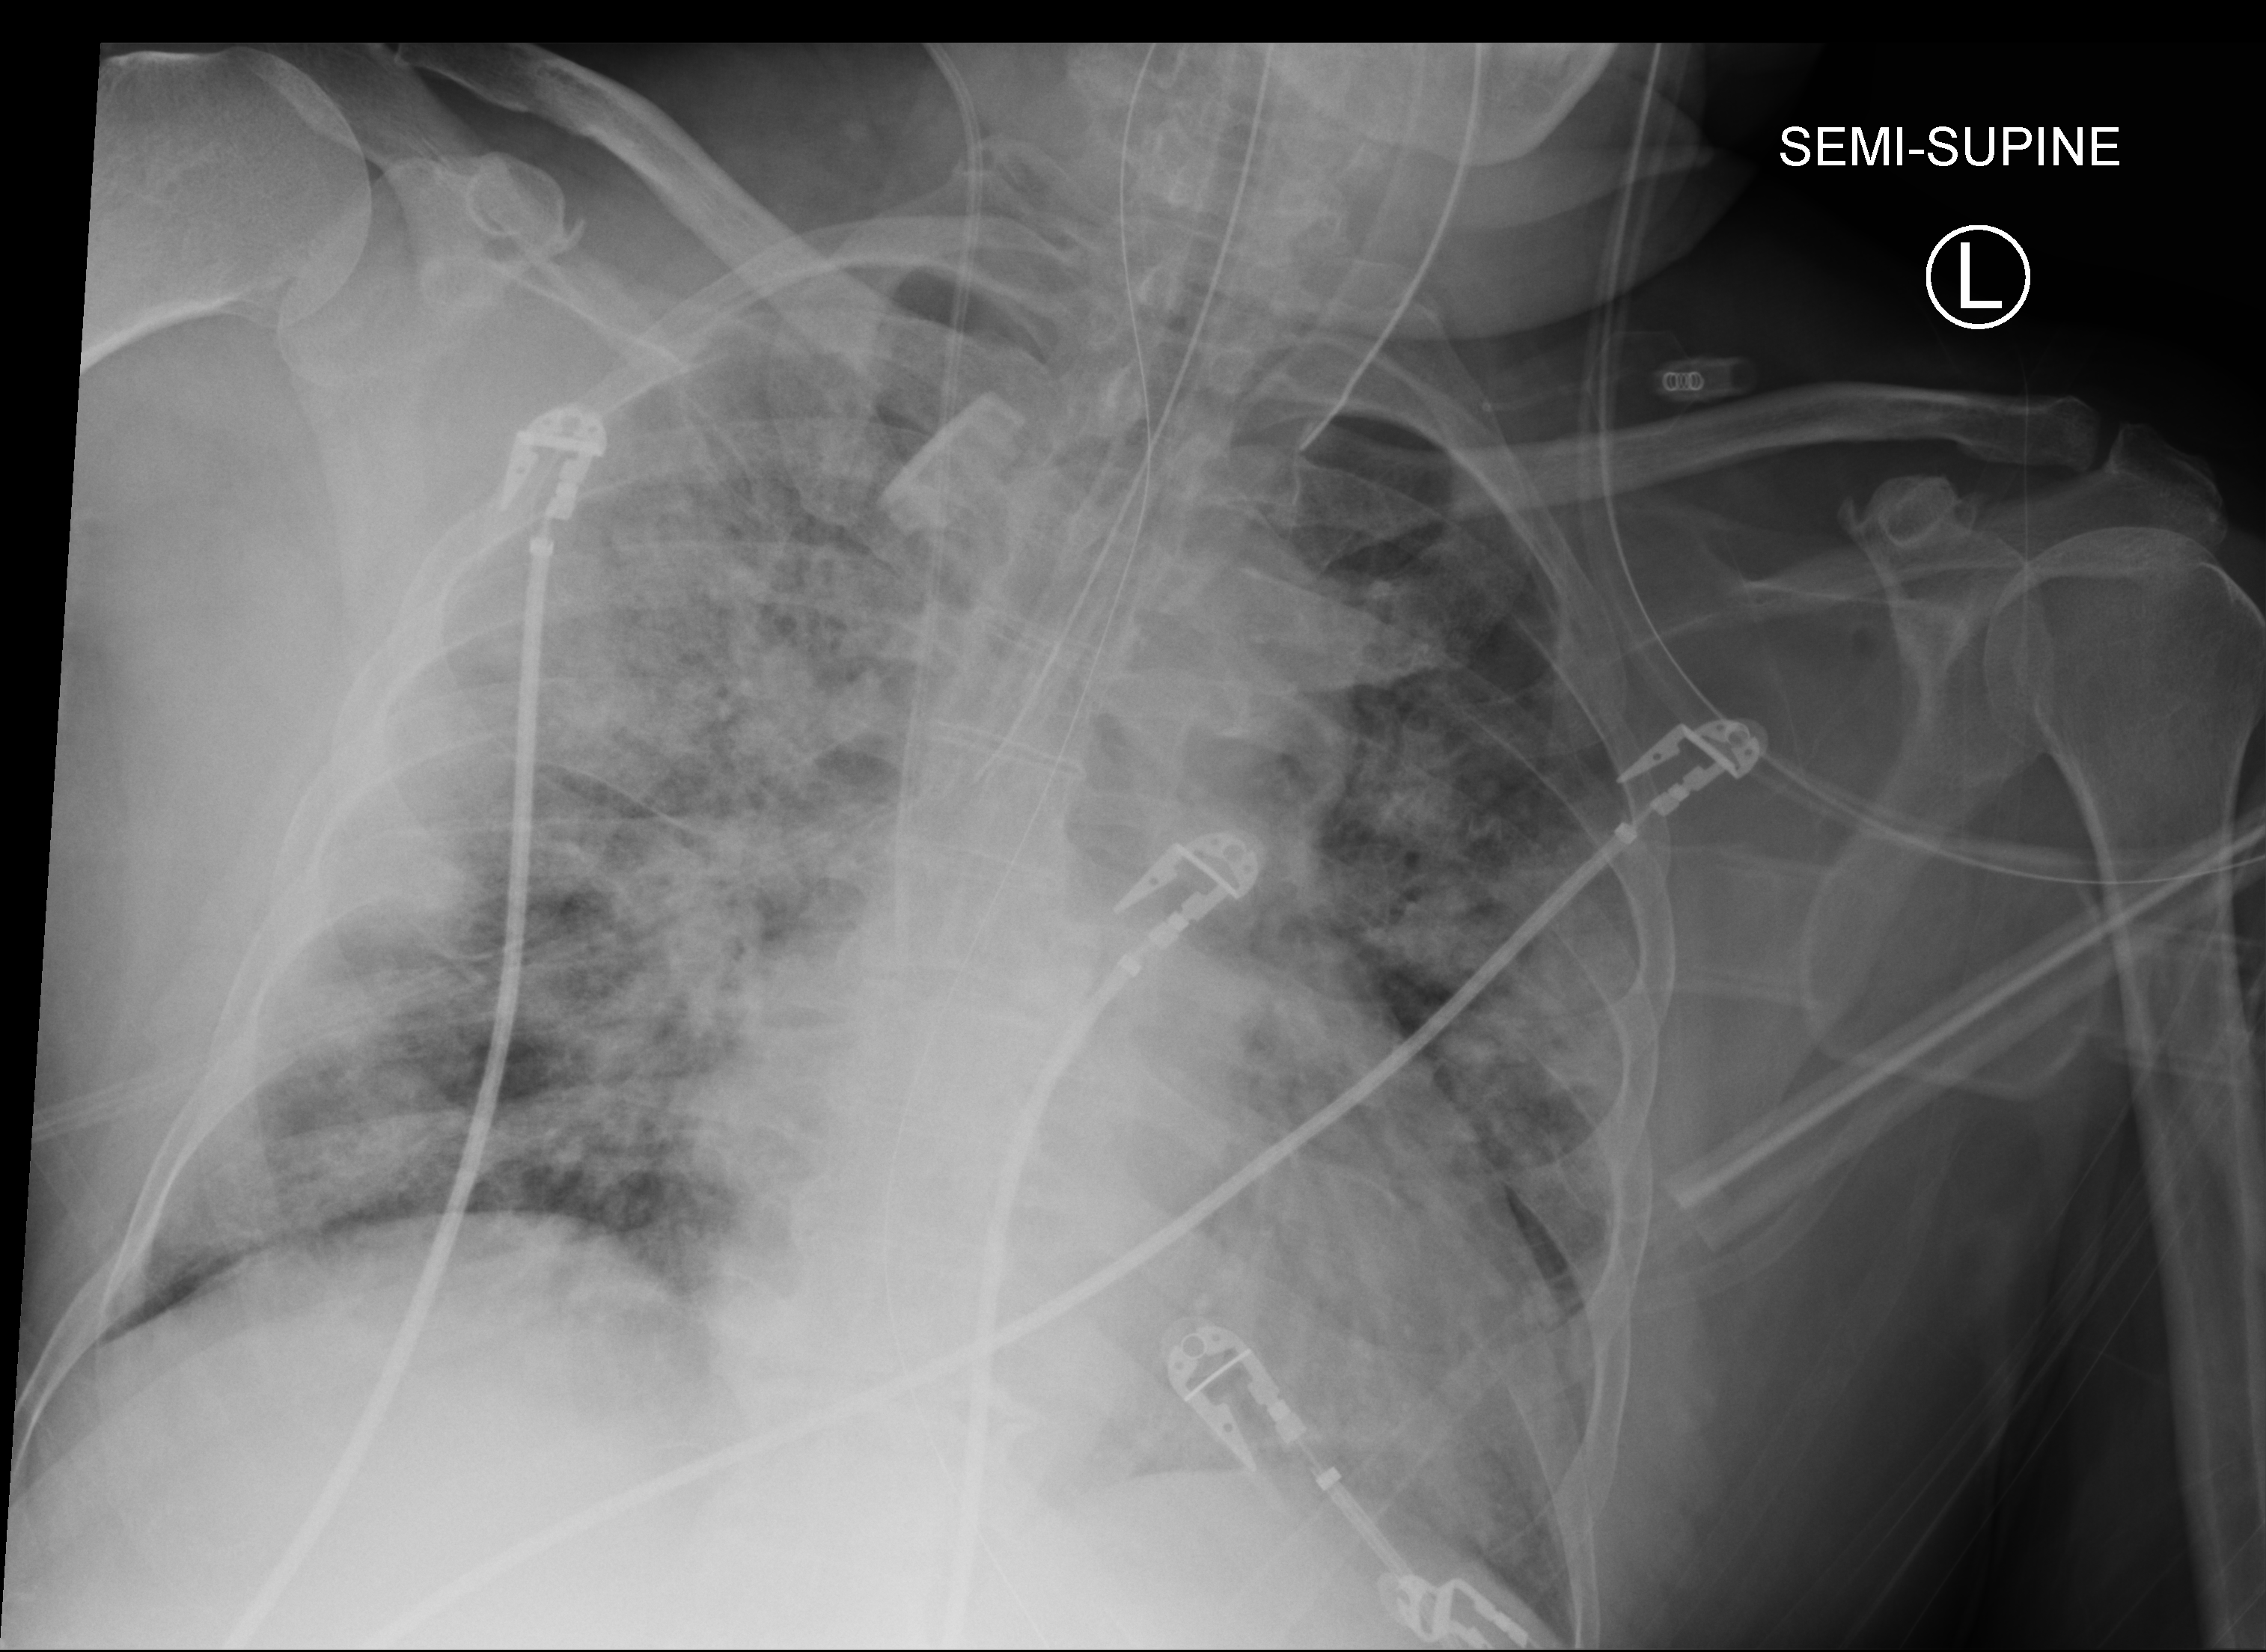
Chest X-ray (portable); anteroposterior (AP) projection. Male patient hospitalised with COVID-19, age 60–74 years.
Hospital-stay facts (about this admission, not read from this image; timing relative to this image not recorded): admitted to intensive care during this hospital stay: yes; mechanically ventilated during this hospital stay: yes.